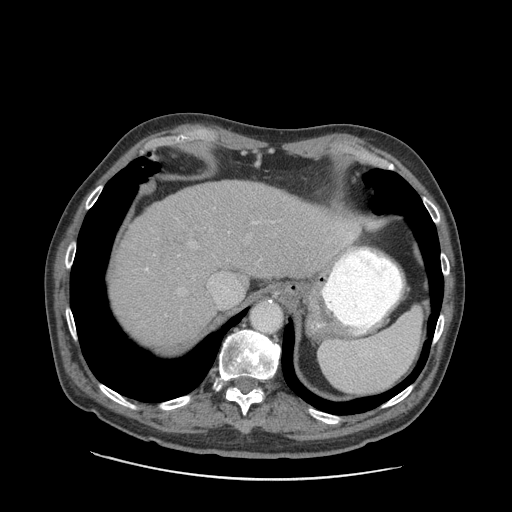
Contrast-enhanced abdominal CT (liver protocol), one axial slice. Slice 71 of 89 in the series (ordered by position). Soft-tissue window (W 400 / L 40 HU). 2.5 mm slice thickness. 512 × 512 image matrix, field of view 420 × 420 mm. Case-level facts recorded for this patient, not image findings: diagnosis: hepatocellular carcinoma (patient treated with transarterial chemoembolisation; whether this scan precedes or follows treatment is not stated here); TNM stage (as recorded): Stage-I; Child-Pugh class: A; tumour differentiation: moderately differentiated; tumour nodularity: uninodular.
Annotated regions visible in this slice (semi-automatic segmentation, software-assisted and operator-edited):
- liver parenchyma outside the tumour (the mass and vessels are separate outlines, so this box may not span the whole liver): bounding box <112,180,360,348> (left, top, right, bottom; pixels)
- liver vessels: <146,219,354,306>